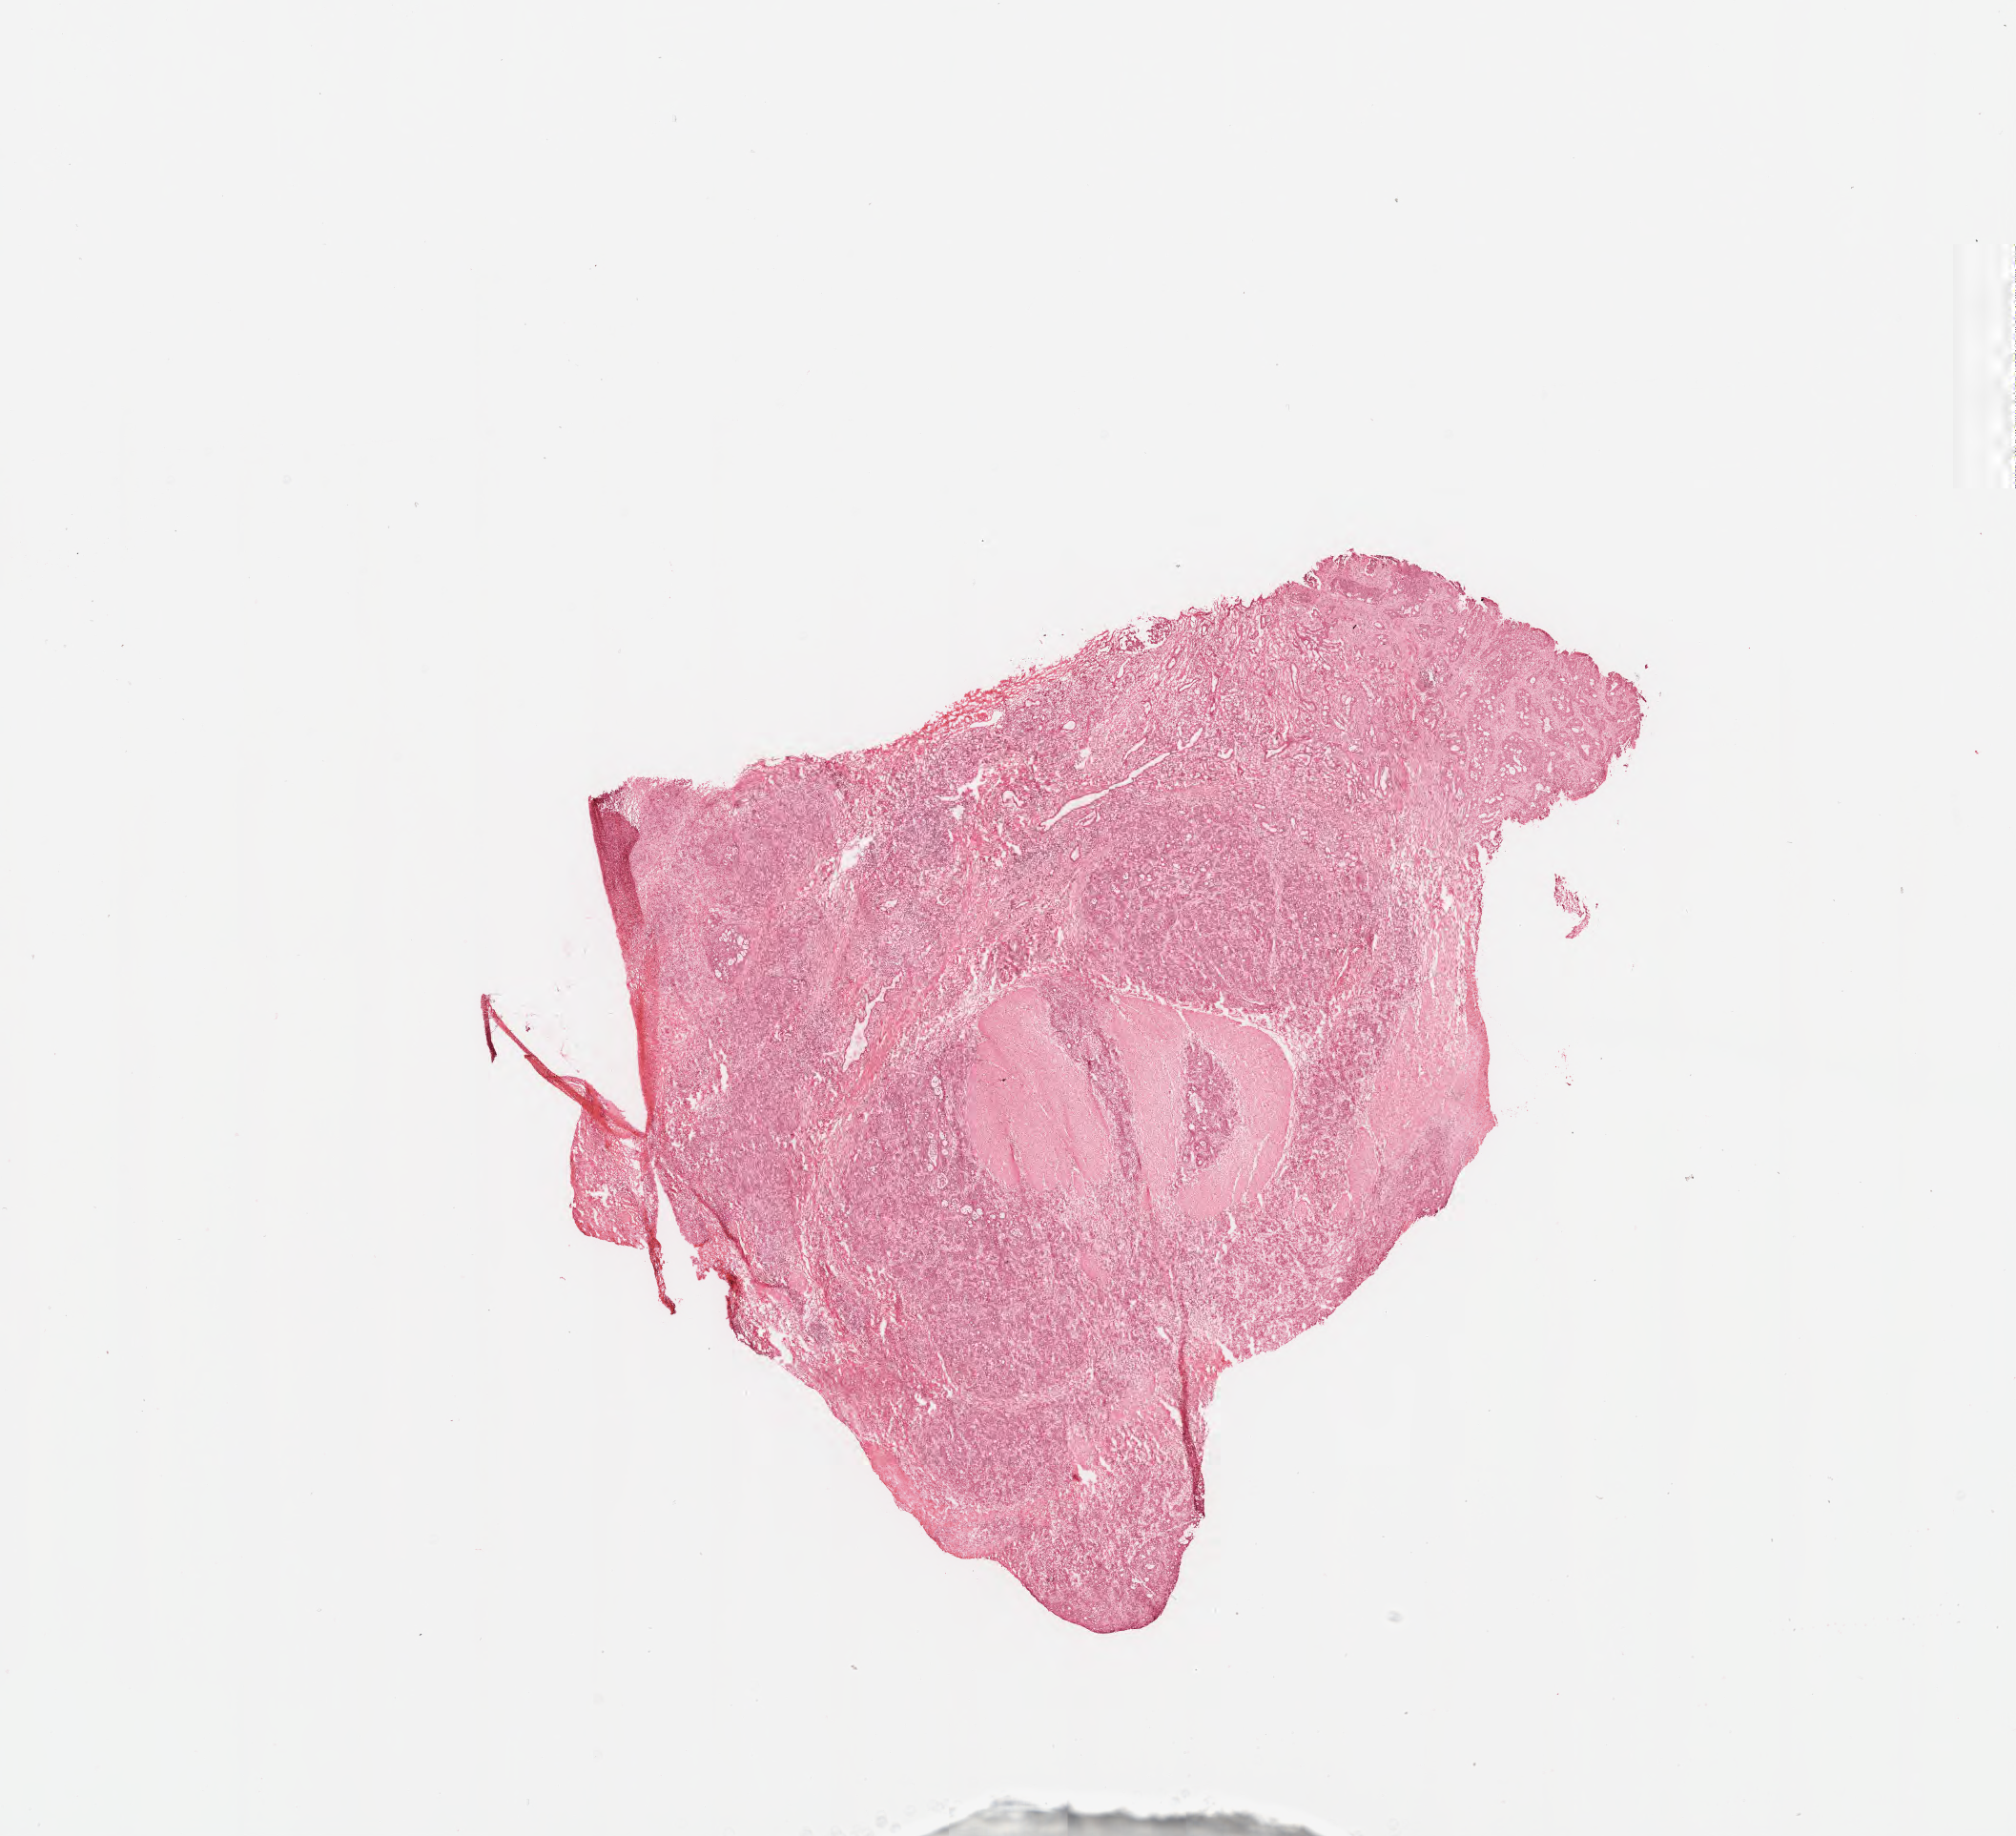
Whole-slide image, haematoxylin and eosin stain, a low-resolution overview of the entire scanned area, about 16.7 x 15.2 mm. Cryosection. Primary tumor. Patient: male, age at initial diagnosis 56 years. Tumor grade: G3 (poorly differentiated). Pathologist review of this section (percent, as recorded): tumor cells 60%, tumor nuclei 90%, stromal cells 20%, necrosis 18%, normal cells 2%. Infiltration values recorded for this section: lymphocyte infiltration 0%, monocyte infiltration 0%, neutrophil infiltration 0%.
AJCC pathologic stage: Stage IIIB. Section: top of the tissue portion. Diagnosis: Adenocarcinoma, metastatic, NOS.